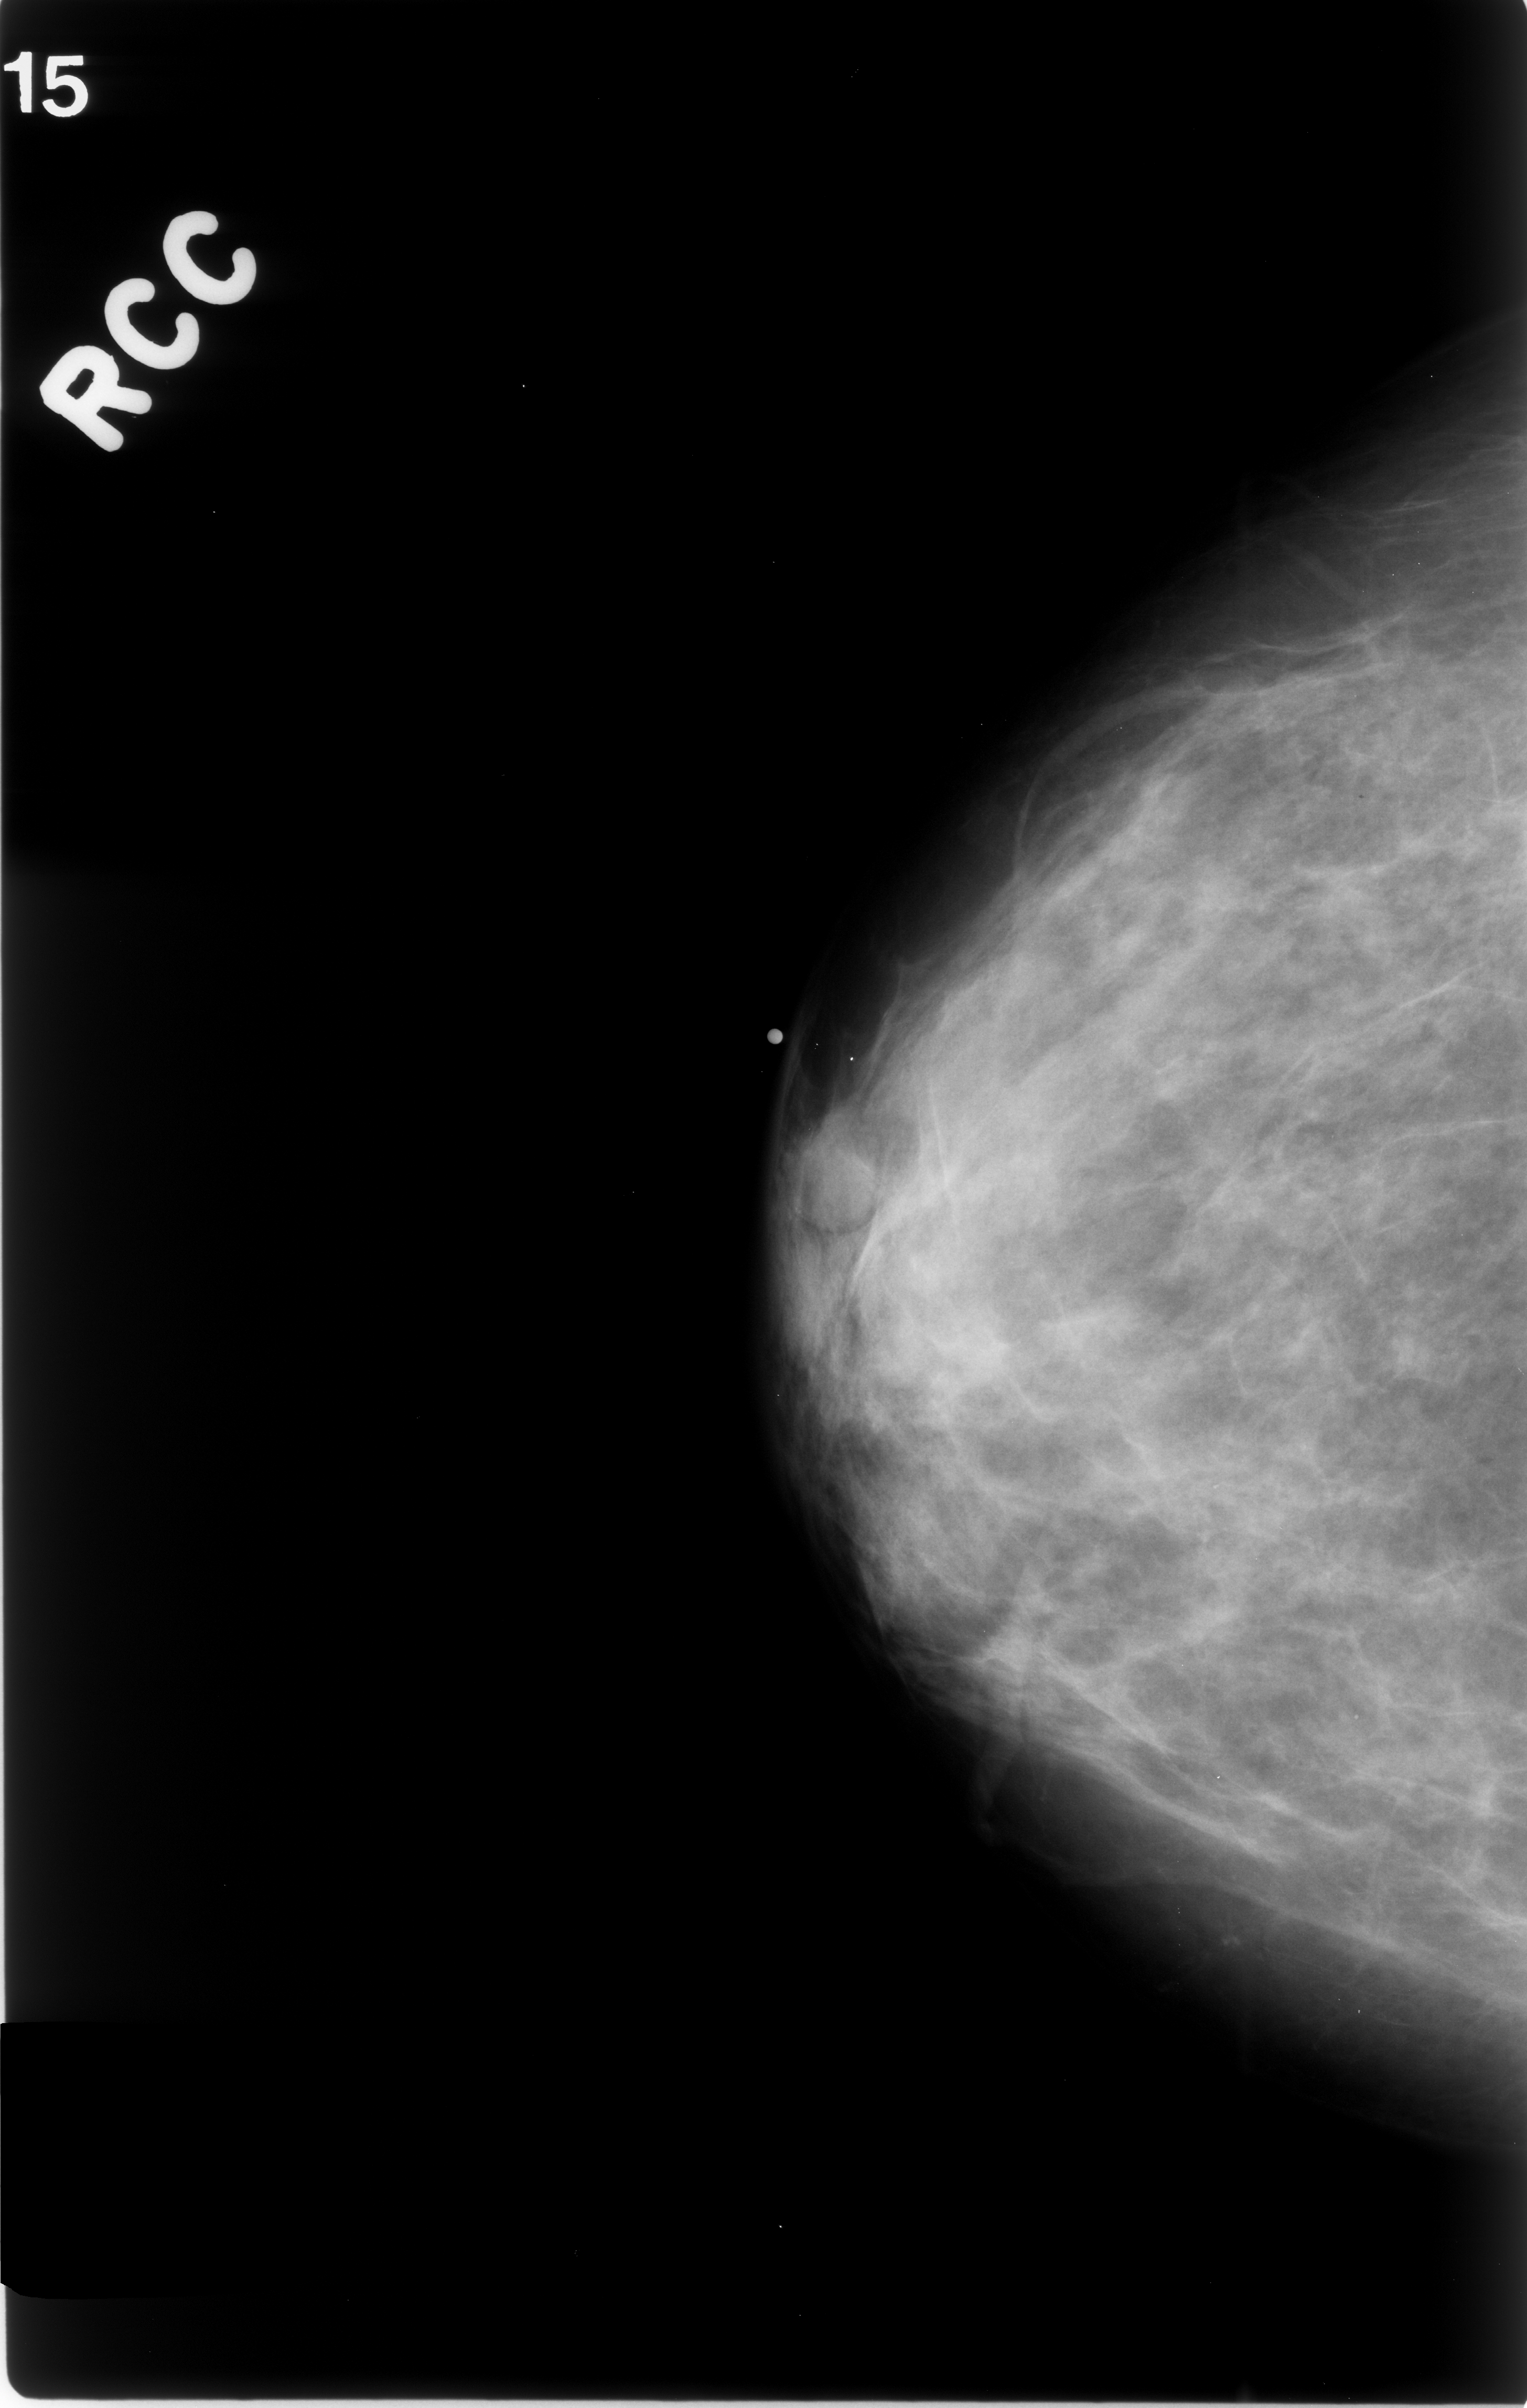
Scanned film-screen mammogram, right breast, craniocaudal (CC) view.
- Mass, shape round, margins circumscribed; BI-RADS assessment category 3; pathology result (as recorded, not read from the image): benign.